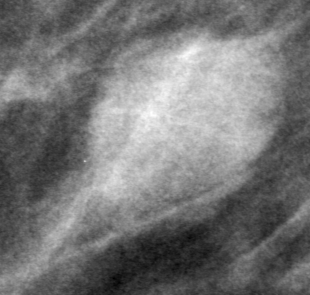
Cropped region of a digitized screen-film mammogram centred on a radiologist-marked abnormality, right breast, MLO view, BI-RADS breast density category 2 (scale 1–4).
Finding: mass, shape oval, margins ill defined; BI-RADS assessment category 0; pathology result (as recorded, not read from the image): benign.